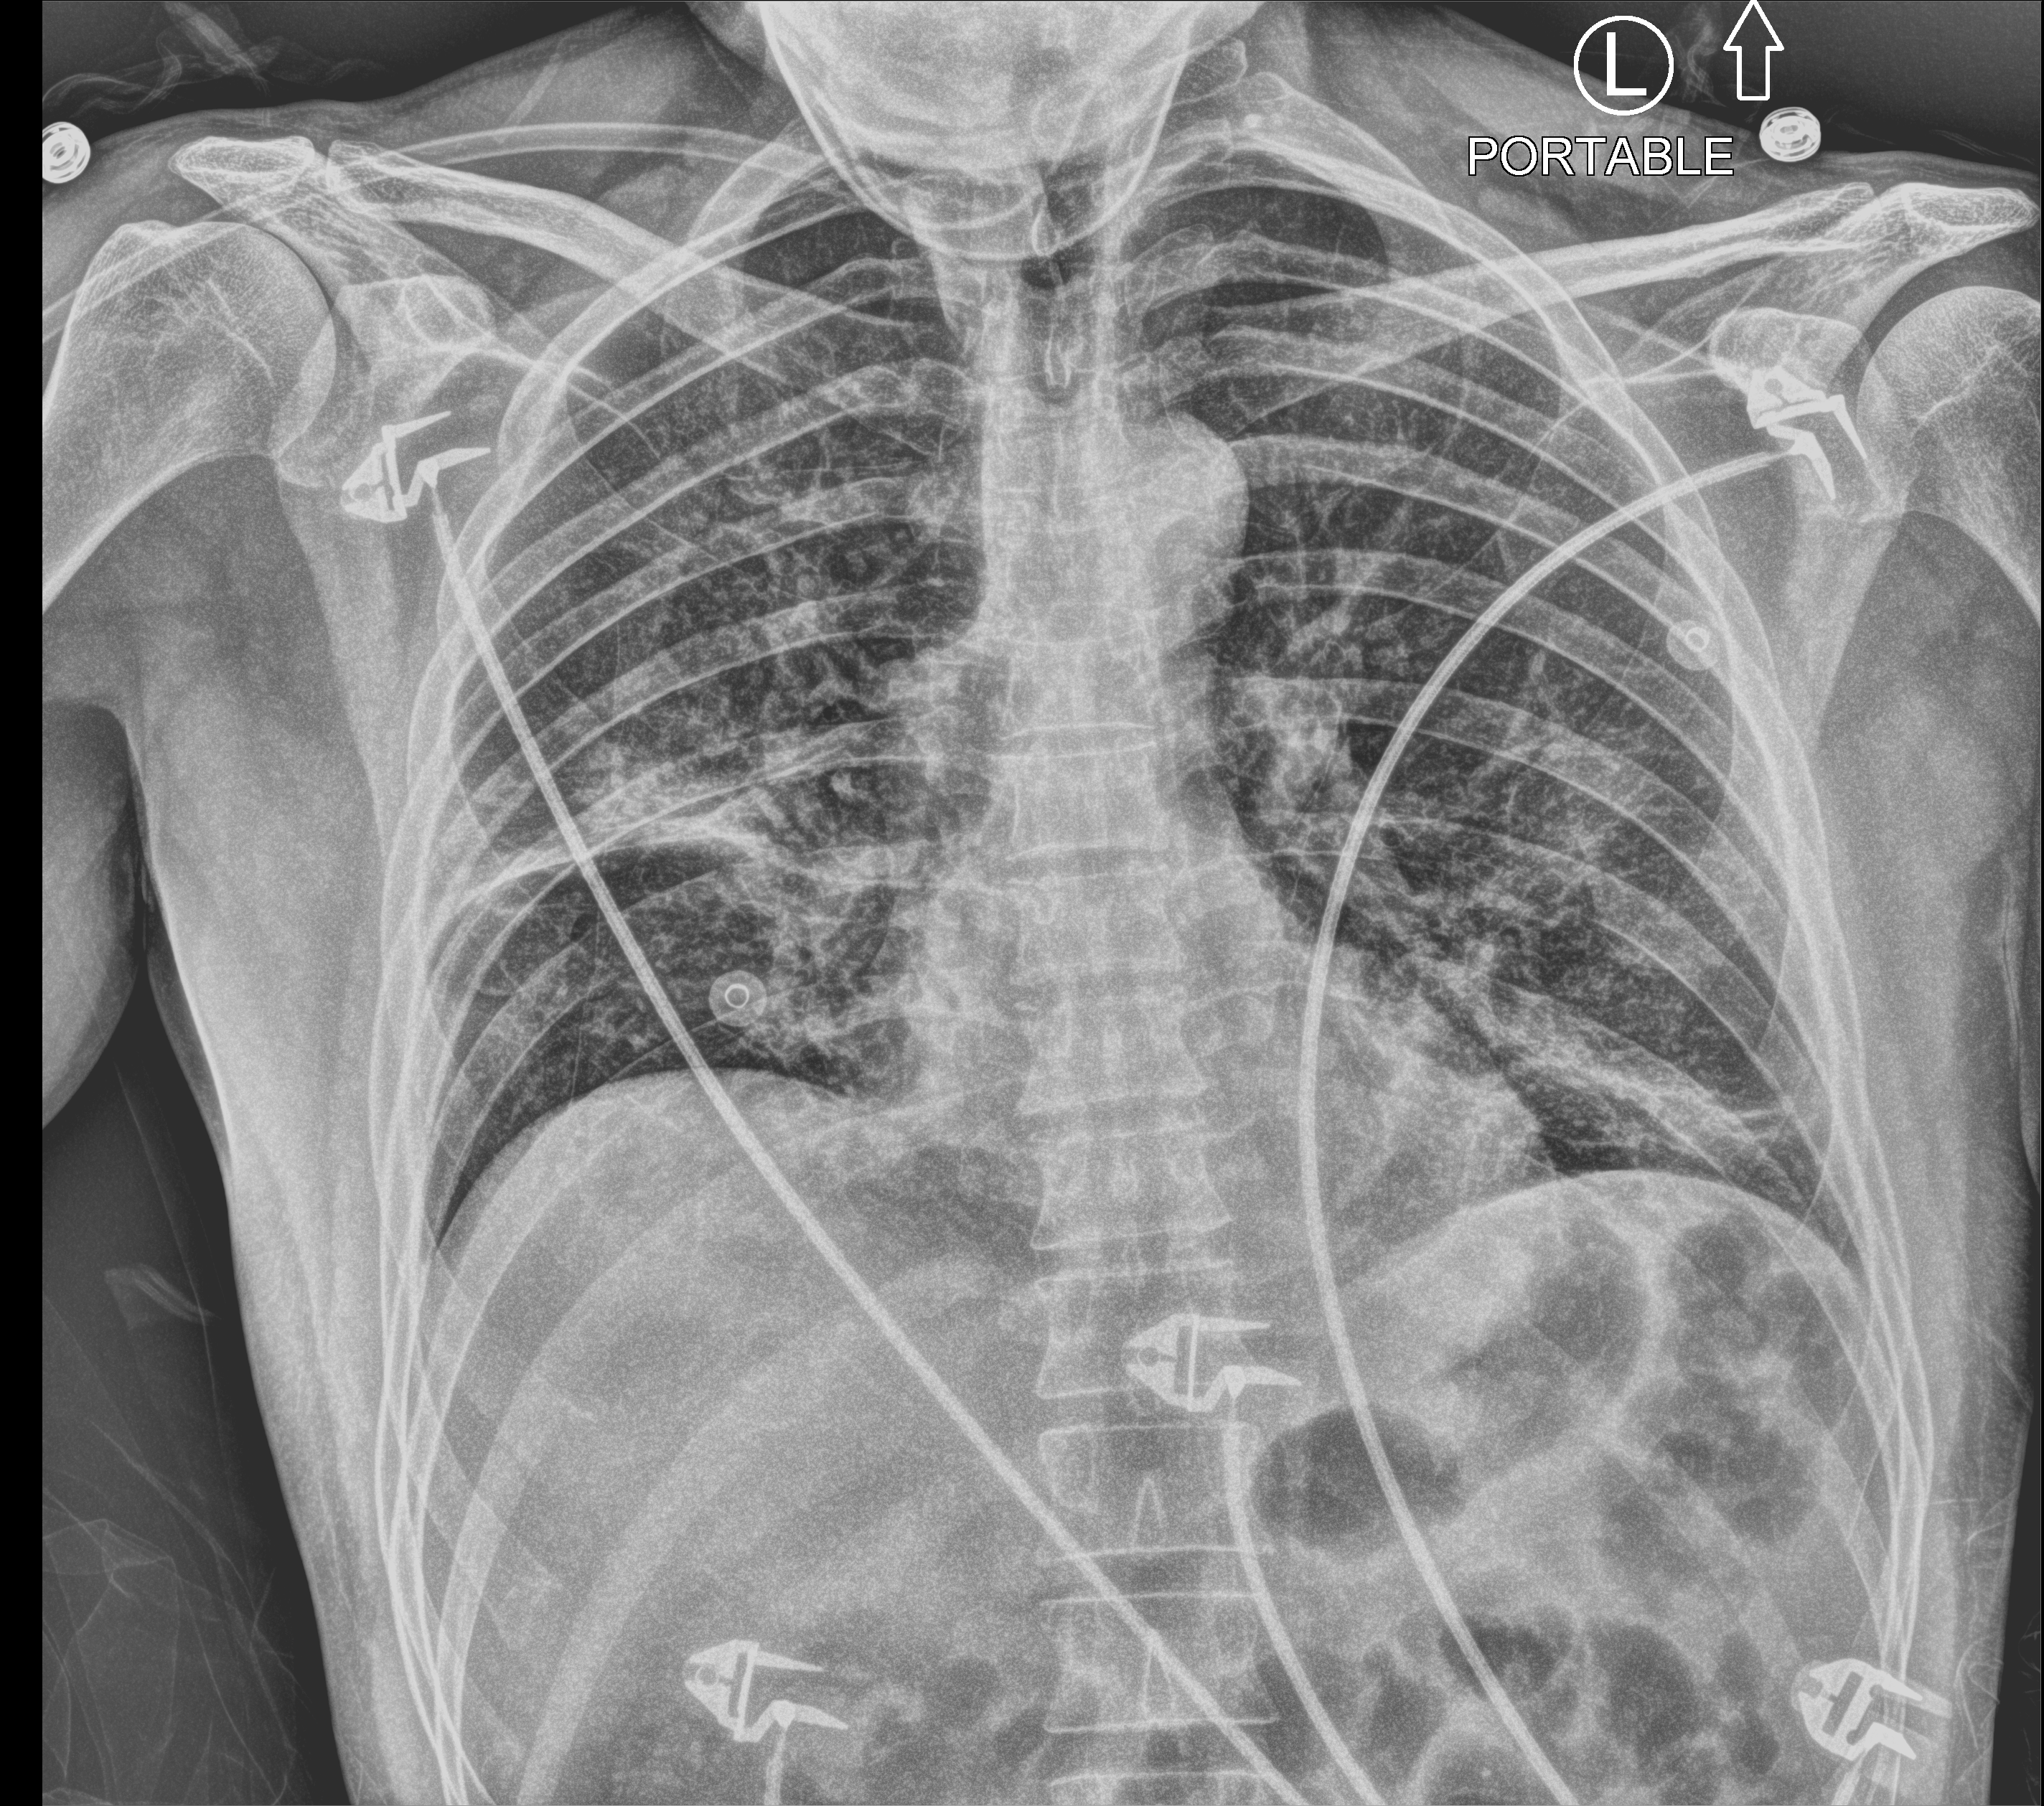
Portable chest radiograph. Male patient hospitalised with COVID-19, age 18–59 years.
From the hospital-stay record, not from the radiograph (when in the stay this image was taken is not recorded):
- mechanically ventilated during this hospital stay: no
- hypertension (admission record): no
- other chronic lung disease (admission record): no